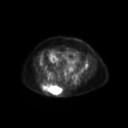
FDG PET of an extremity soft-tissue mass (from a PET/CT study), one axial slice. Position 73 of 267 along the scan axis. 3.27 mm slice thickness. 128 × 128 image matrix, field of view 600 × 600 mm. Patient: female, 60 years. Case-level facts recorded for this patient, not image findings: histological type: spindle cell suggestive of myxofibrosarcoma; grade: intermediate; site of the primary tumour: right buttock.
Annotated regions visible in this slice (expert contour drawn on MRI and transferred to this co-registered scan by the dataset authors):
- gross tumour volume (mass): box from (x=41, y=85) to (x=63, y=96) px